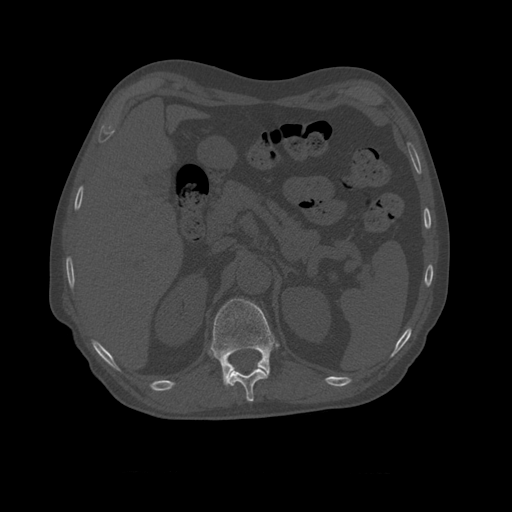
CT including the spine, one axial slice; slice 389 of 450 in the series (ordered by position); bone window (W 1800 / L 400 HU); 1.25 mm slice thickness; 512 × 512 image matrix, field of view 405 × 405 mm. Patient age 75 years. From the clinical record (not read from this slice): primary cancer: prostate.
Structures marked on this image (semi-automatic segmentation, software-assisted and operator-edited):
- T10 vertebra: bounding box [x1, y1, x2, y2] px = [228, 368, 269, 402]
- T11 vertebra: [211, 299, 276, 387]